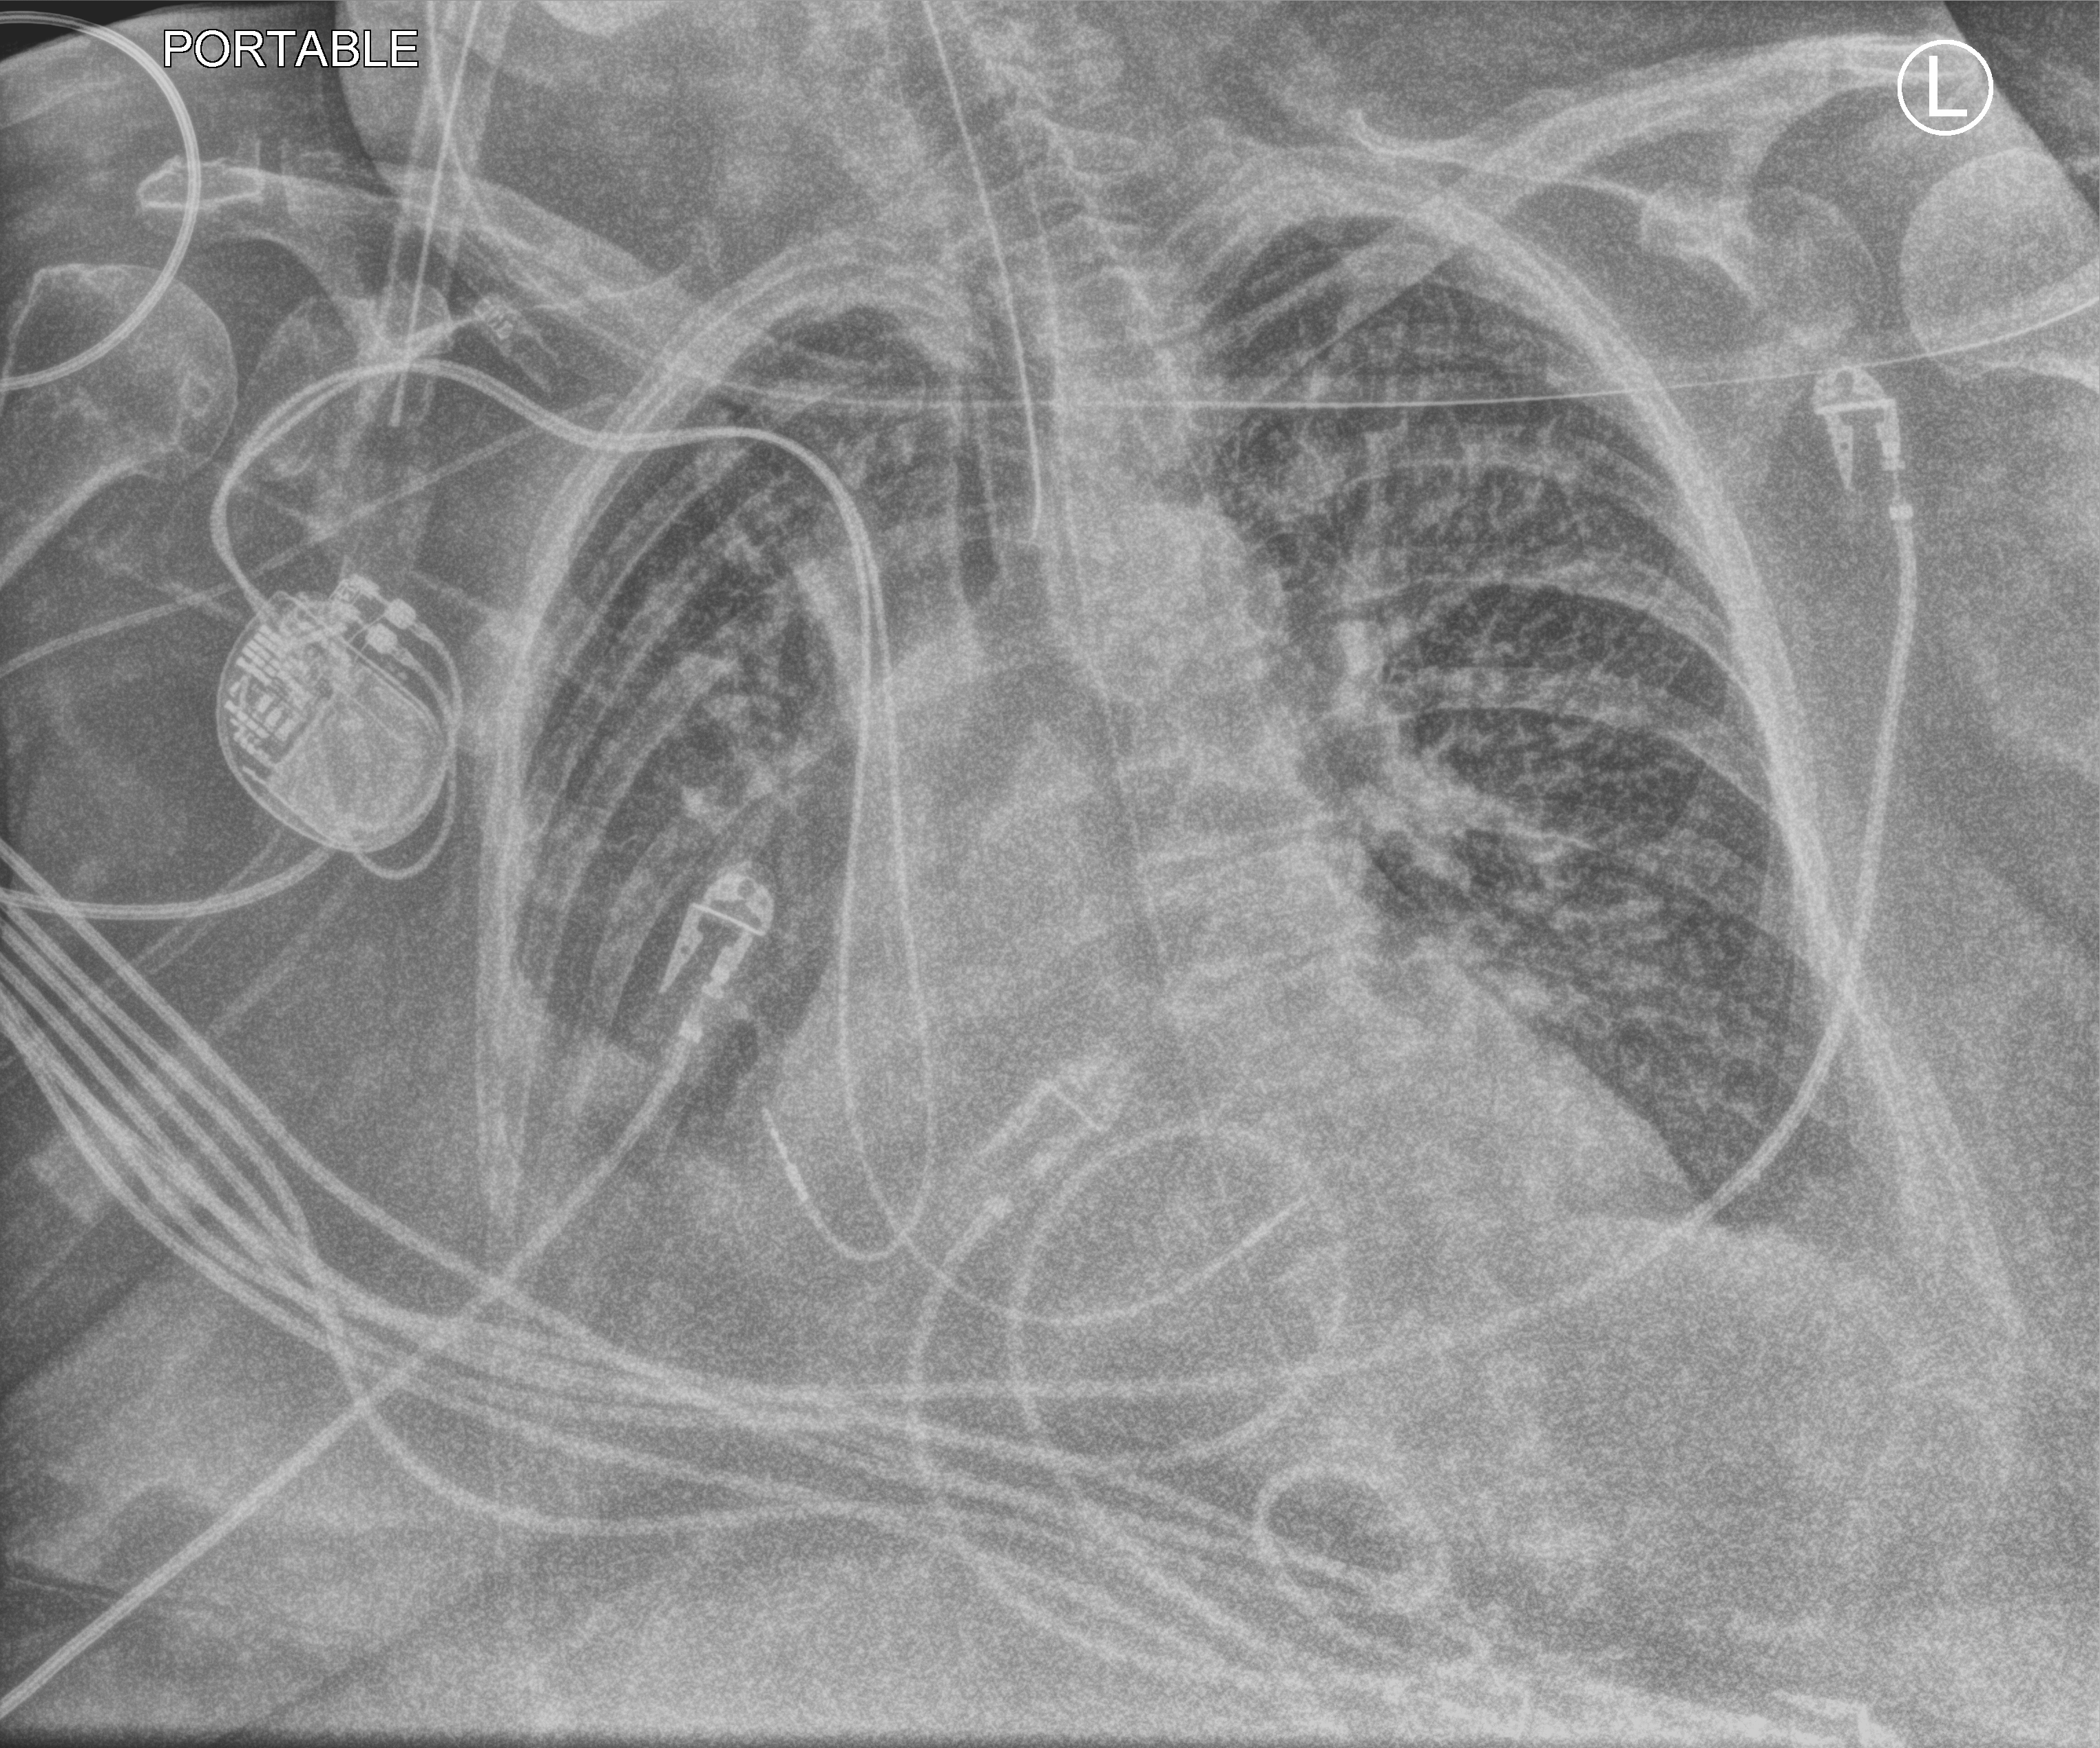
Portable chest radiograph; anteroposterior (AP) projection. Female patient hospitalised with COVID-19, age 75–90 years.
From the hospital-stay record, not from the radiograph (when in the stay this image was taken is not recorded):
- admitted to intensive care during this hospital stay: yes